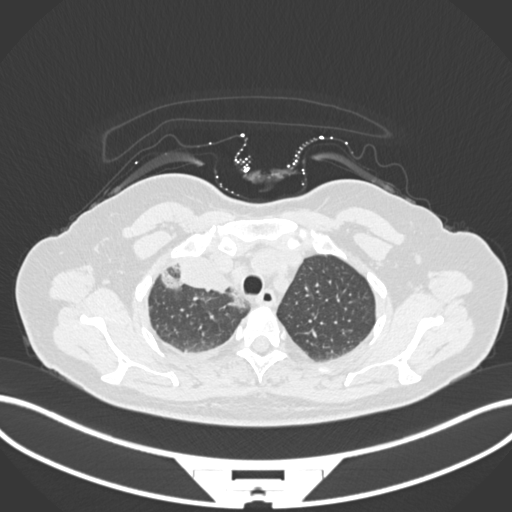
Chest CT, one axial slice. Slice 137 of 172 in the series (ordered by position). 120 kVp. Lung window (W 1500 / L -600 HU). 1 mm slice thickness. 512 × 512 image matrix, field of view 400 × 400 mm. Patient: female, 52 years. From the clinical record (not read from this slice): clinical TNM (as recorded): T3 N1 M1.
Annotated regions visible in this slice (bounding box drawn by a radiologist):
- lung tumour (recorded histology: adenocarcinoma): bounding box [x1, y1, x2, y2] px = [158, 254, 233, 296]